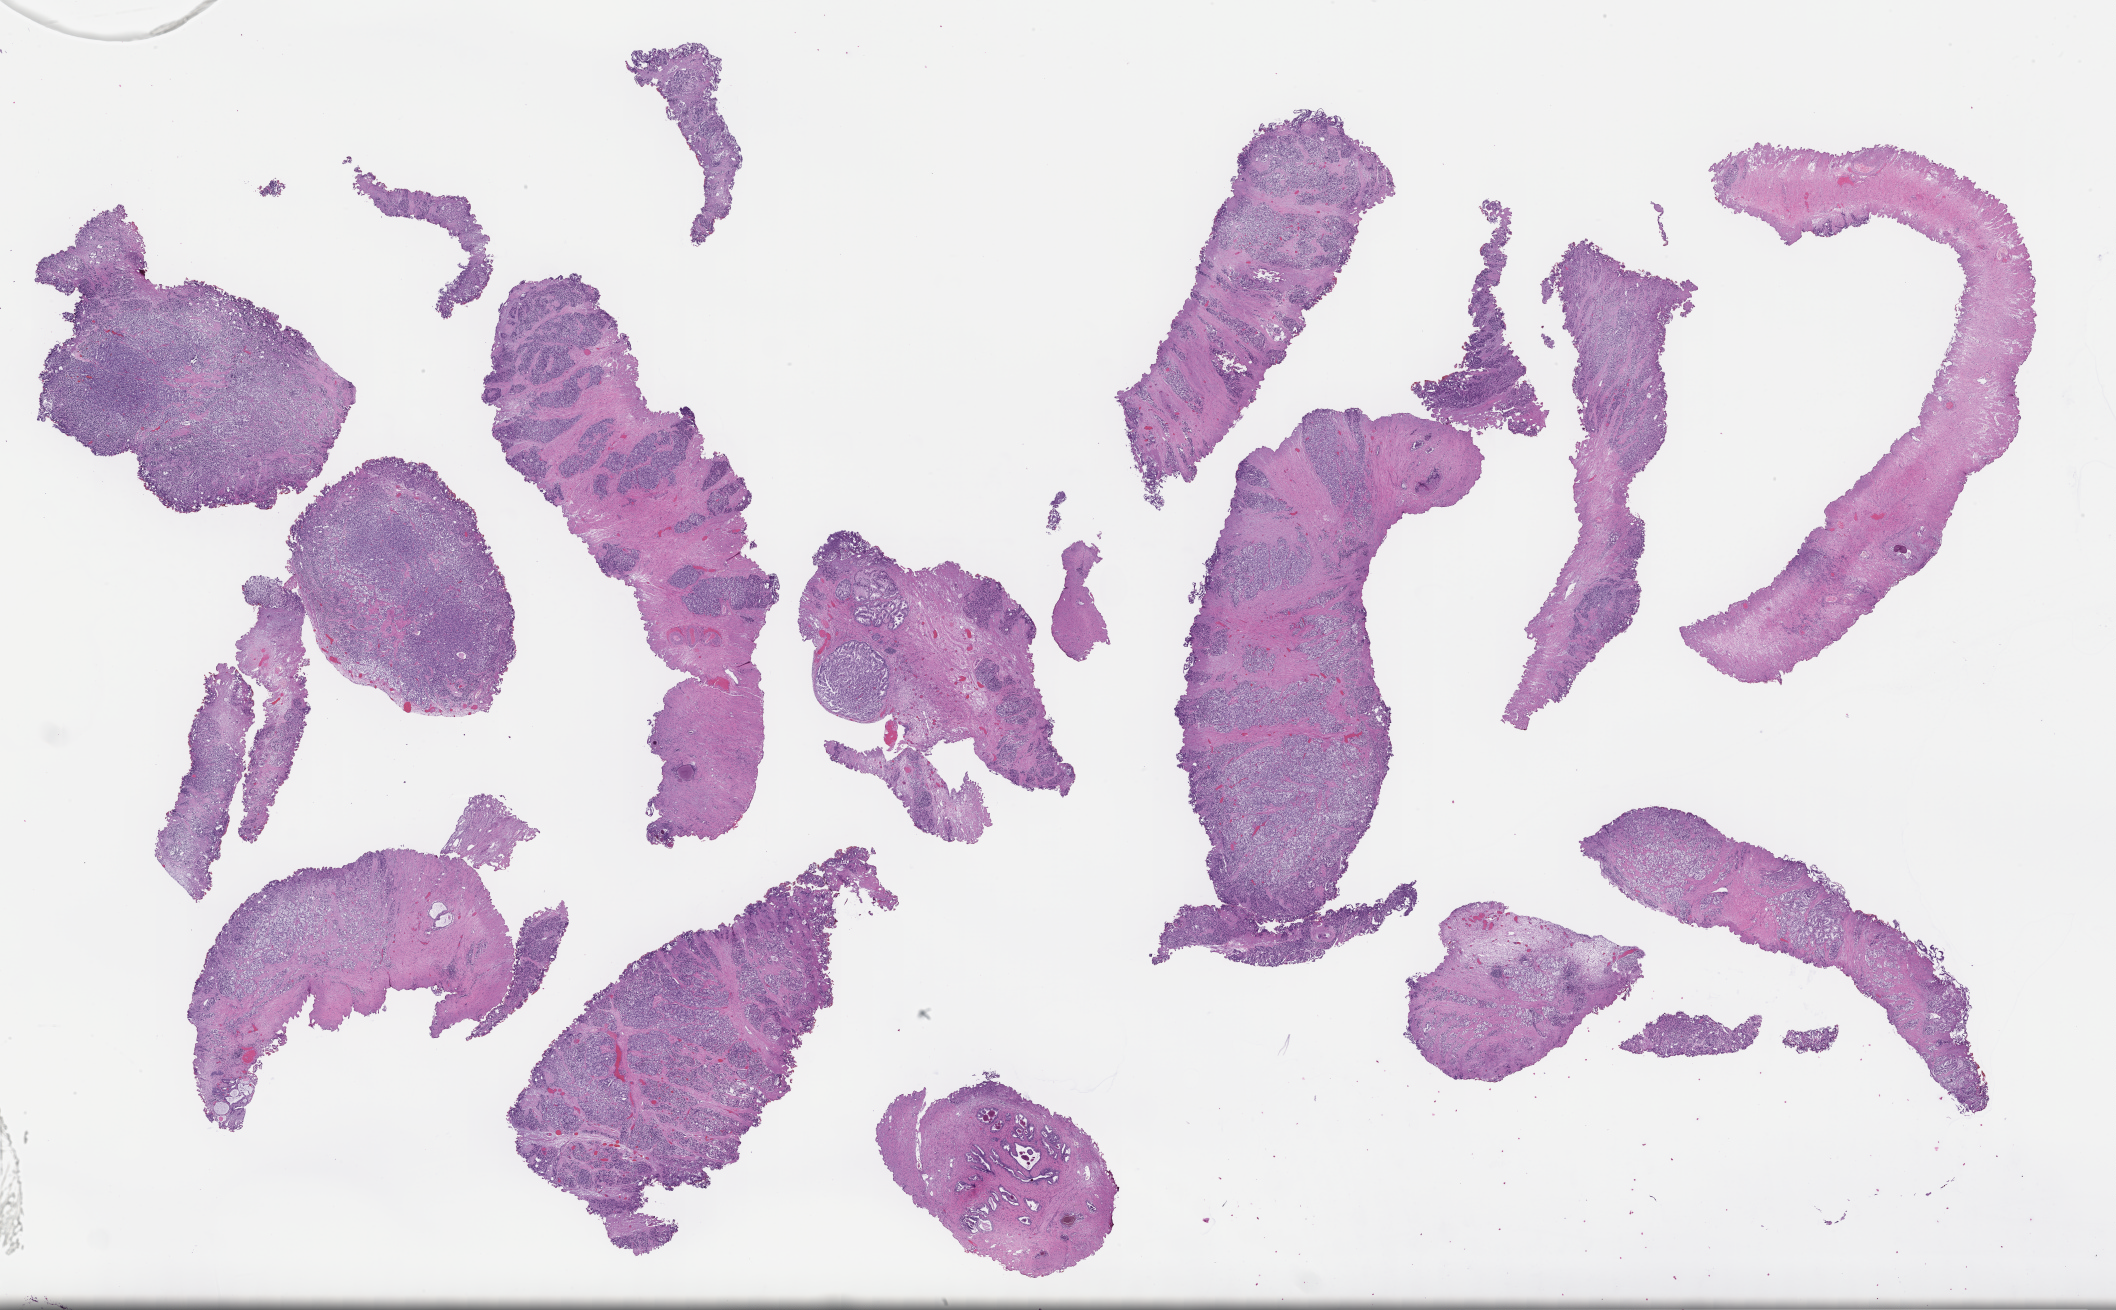
Haematoxylin and eosin whole-slide image, a low-resolution overview of the entire scanned area, about 34.2 x 21.2 mm. Formalin-fixed paraffin-embedded section. Site: prostate. Archival tissue. Patient sex: male.
This section: primary tumour tissue. Diagnosis: Prostate Carcinoma.